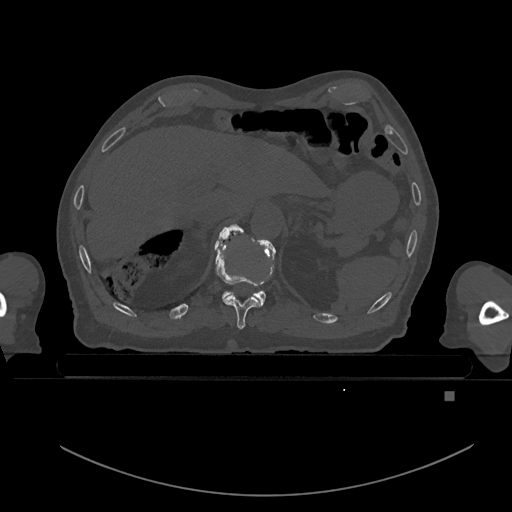
CT including the spine, one axial slice; slice 65 of 969 in the series (ordered by position); bone window (W 1800 / L 400 HU); 512 × 512 image matrix, field of view 456 × 456 mm. Patient: male, 82 years. From the clinical record (not read from this slice): primary cancer: prostate; vertebrae with lytic lesions (as recorded): T11, T9, T8, T2.
Structures marked on this image (semi-automatic segmentation, software-assisted and operator-edited):
- T10 vertebra: box from (x=214, y=225) to (x=261, y=330) px
- T11 vertebra: (x=218, y=223)–(x=276, y=306)